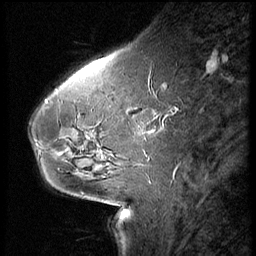
Breast MRI (dynamic contrast-enhanced), one sagittal slice. Position 21 of 66 along the scan axis. 3 images stored at this slice position (order not interpretable as contrast timing). 1.5 T. TE 4.2 ms, TR 8.9 ms. 256 × 256 image matrix, field of view 200 × 200 mm. Female patient, age 54 years. Case-level facts recorded for this patient, not image findings: setting: breast cancer imaged before/during neoadjuvant chemotherapy; receptor status: HR-positive, HER2-negative.
Annotated regions visible in this slice (semi-automatic segmentation, software-assisted and operator-edited):
- analysis volume of interest (the breast-tissue region the enhancement analysis was run in; not a lesion): bounding box <61,104,146,171> (left, top, right, bottom; pixels)
- tumour enhancement mask (voxels above the 140 % enhancement threshold inside the analysis volume of interest): <116,108,141,167>